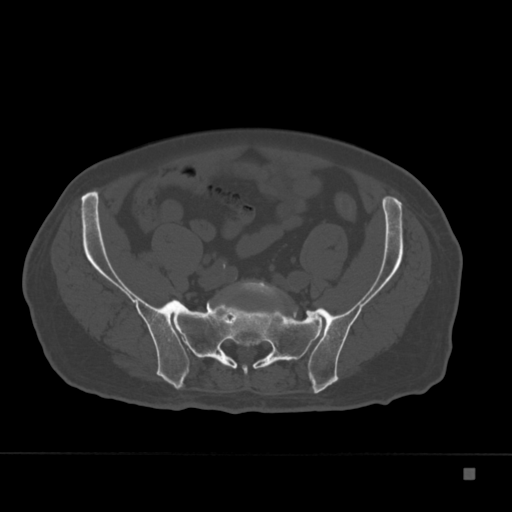
CT including the spine, one axial slice; slice 6 of 332 in the series (ordered by position); reconstruction kernel Br40s; 120 kVp; bone window (W 1800 / L 400 HU); 512 × 512 image matrix, field of view 389 × 389 mm. Patient: male, 72 years. From the clinical record (not read from this slice): primary cancer: skeletal.
Outlined on this slice (semi-automatic segmentation, software-assisted and operator-edited):
- L5 vertebra: bounding box (x1, y1, x2, y2) in pixels: (231, 281, 278, 302)